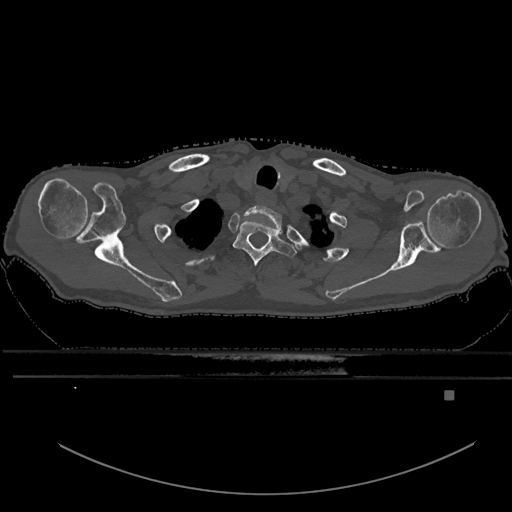
CT including the spine, one axial slice. Slice 540 of 969 in the series (ordered by position). Bone window (W 1800 / L 400 HU). 0.5 mm slice thickness. 512 × 512 image matrix, field of view 456 × 456 mm. Male patient, age 82 years. From the clinical record (not read from this slice): primary cancer: prostate; vertebrae with lytic lesions (as recorded): T11, T9, T8, T2.
Structures marked on this image (semi-automatically segmented with operator editing):
- T1 vertebra: bounding box (x1, y1, x2, y2) in pixels: (233, 220, 296, 267)